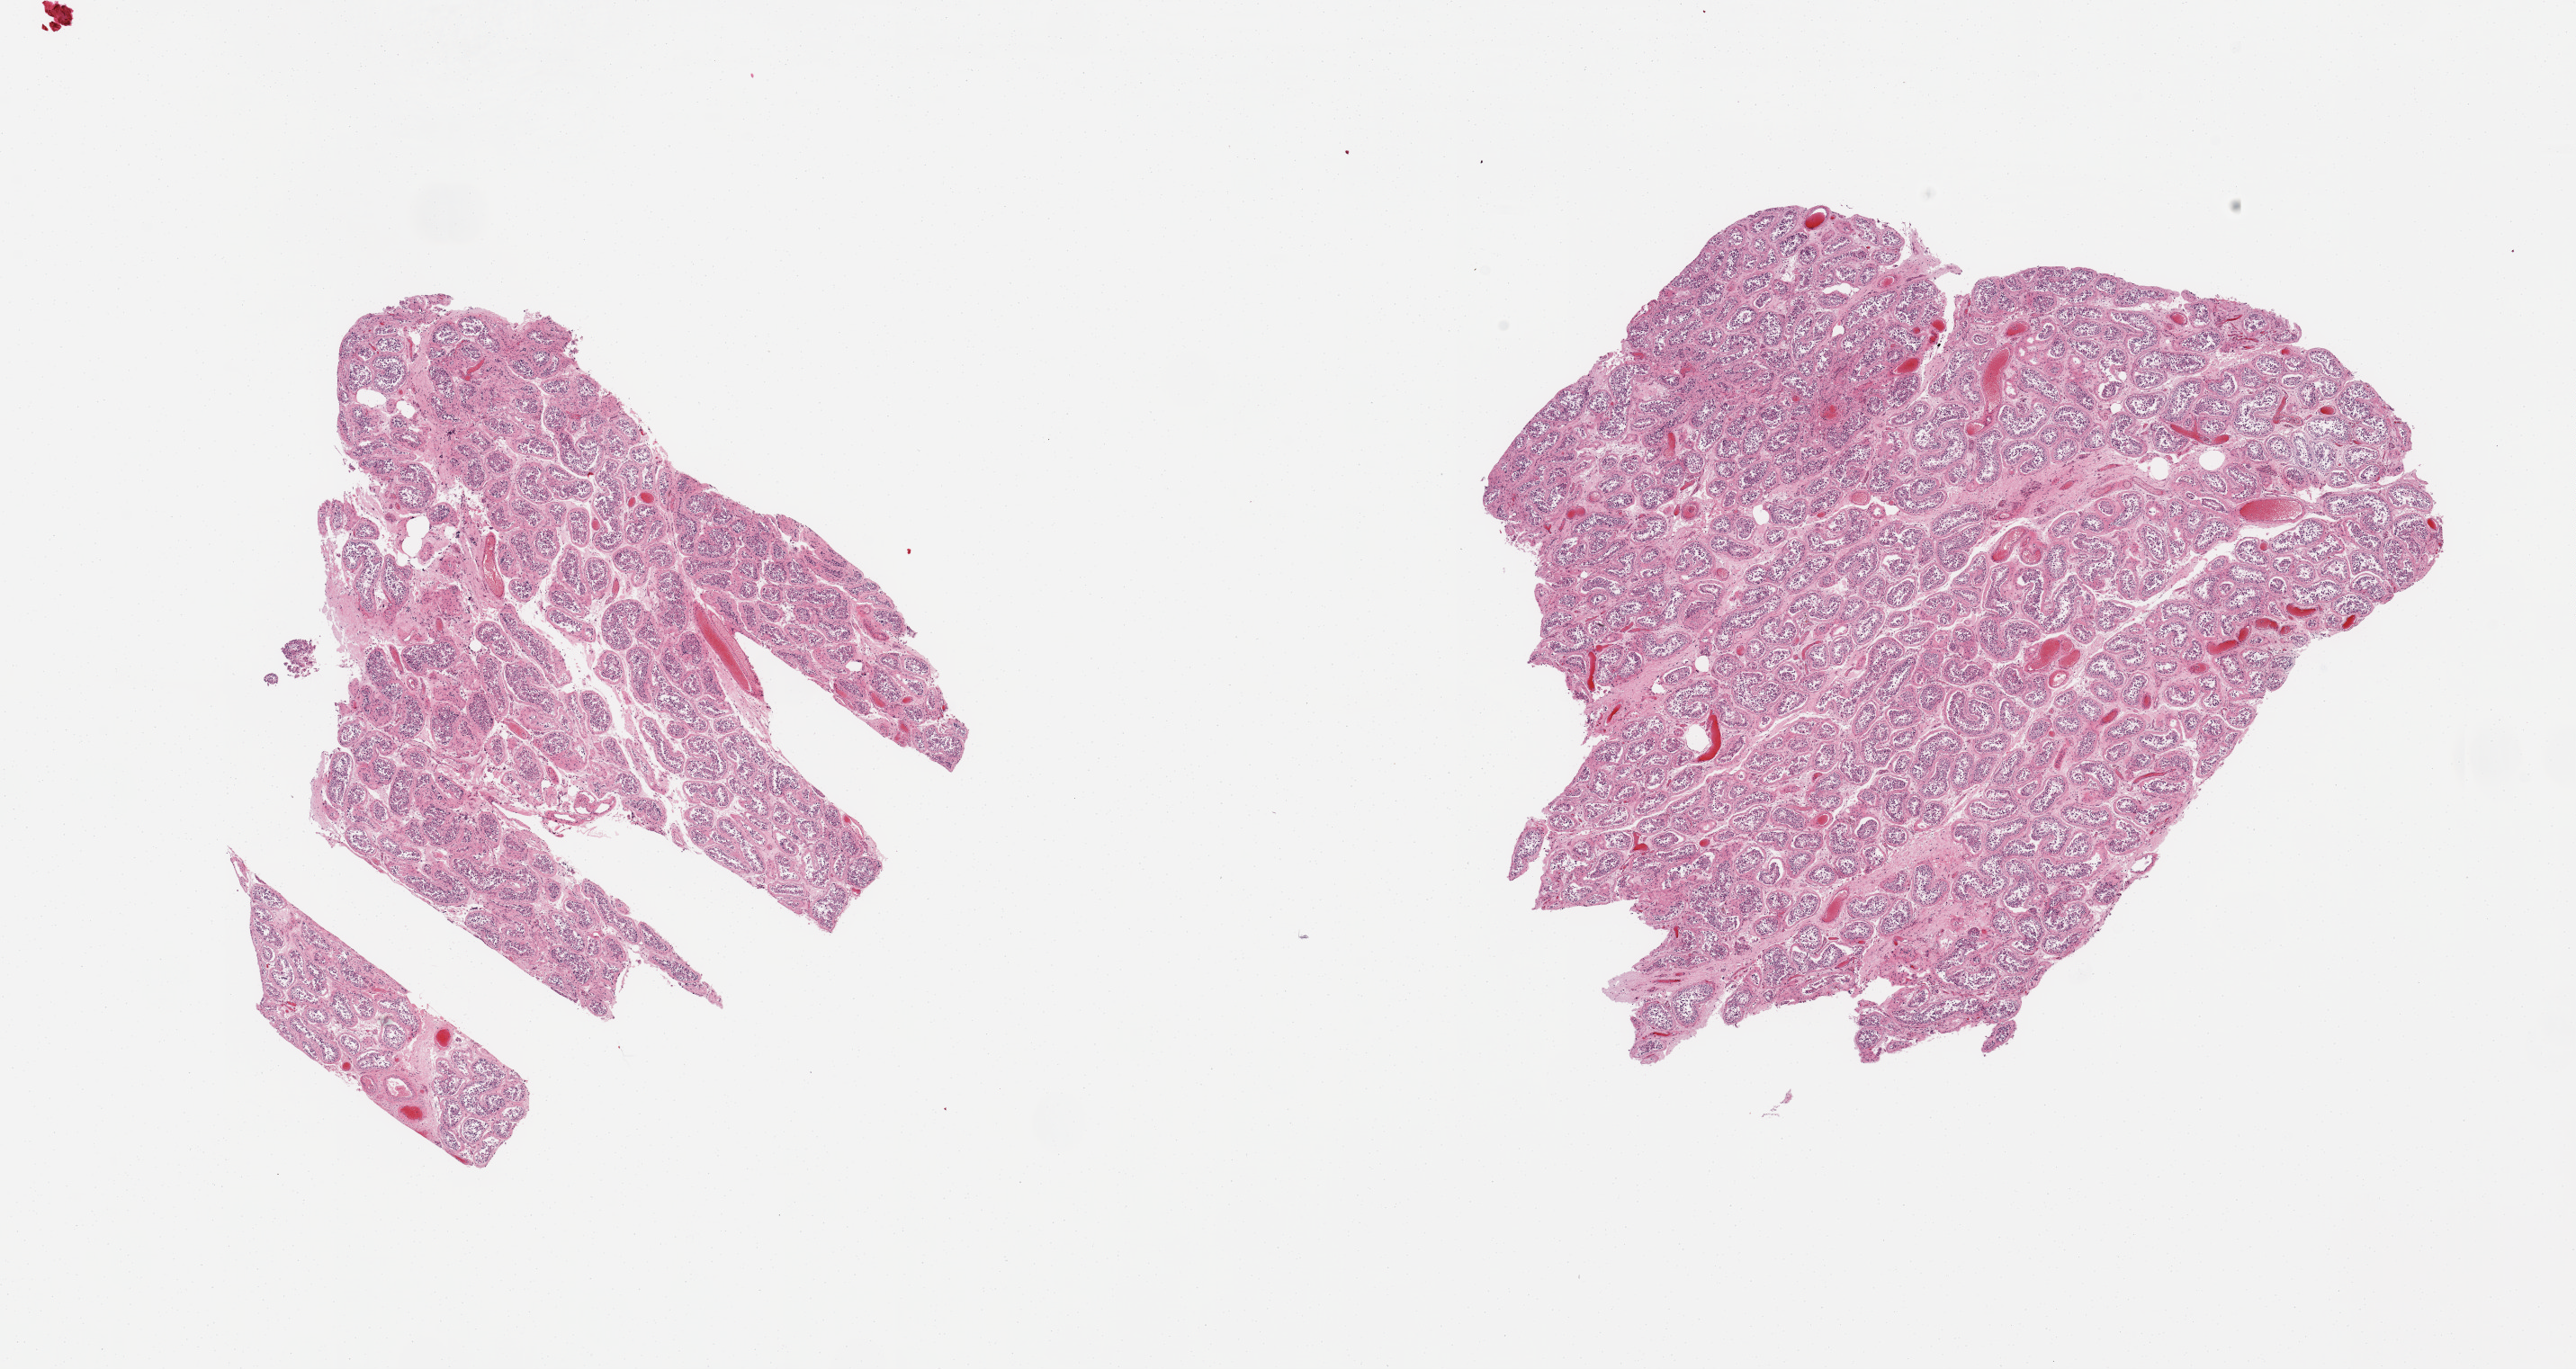
Digitized H&E-stained section — low-resolution overview of the scanned area, about 22.6 x 12.0 mm (from a 20x scan); PAXgene-fixed, paraffin-embedded tissue; target tissue: testis; donor tissue sample. Donor: male.
Reviewer comment on this tissue sample: 2 pieces; reduced mature spermatogenesis.